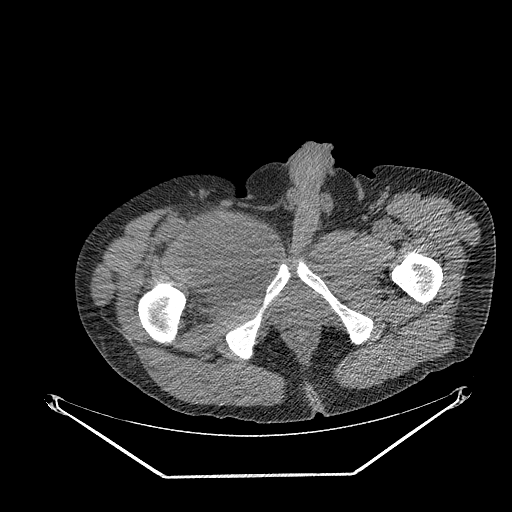
CT of an extremity soft-tissue mass (from a PET/CT study), one axial slice. Position 289 of 311 along the scan axis. Reconstruction kernel STANDARD. Soft-tissue window (W 400 / L 40 HU). 3.75 mm slice thickness. 512 × 512 image matrix, field of view 500 × 500 mm. Male patient. From the clinical record (not read from this slice): histological type: undifferentiated - pleiomorphic; grade: high; site of the primary tumour: right thigh.
Annotated regions visible in this slice (expert contour drawn on MRI and transferred to this co-registered scan by the dataset authors):
- gross tumour volume including surrounding oedema: box from (x=206, y=214) to (x=257, y=254) px
- gross tumour volume (mass): (x=212, y=222)–(x=245, y=250)